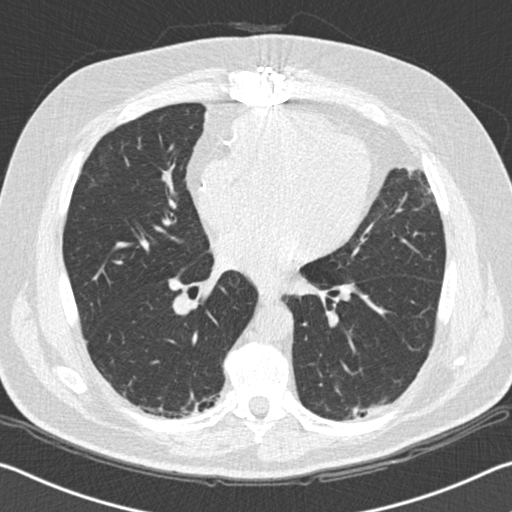
Low-dose screening chest CT, one axial slice. Slice 85 of 172 in the series (ordered by position). Lung window (W 1500 / L -600 HU). 2 mm slice thickness. 512 × 512 image matrix, field of view 340 × 340 mm.
Structures marked on this image (expert manual segmentation):
- lesion 1 (tumor, lower lobe of left lung): bounding box (x1, y1, x2, y2) in pixels: (352, 406, 368, 419)